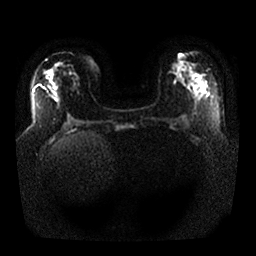
Breast MRI, one axial slice; slice 12 of 25 in the series (ordered by position); diffusion-weighted series; image 2 of 4 stored at this slice position (different b-values; order by instance number); 1.5 T; 256 × 256 image matrix, field of view 350 × 350 mm. Female patient.
Outlined on this slice (manually delineated by an expert):
- tumour on diffusion-weighted imaging: box from (x=192, y=84) to (x=198, y=92) px